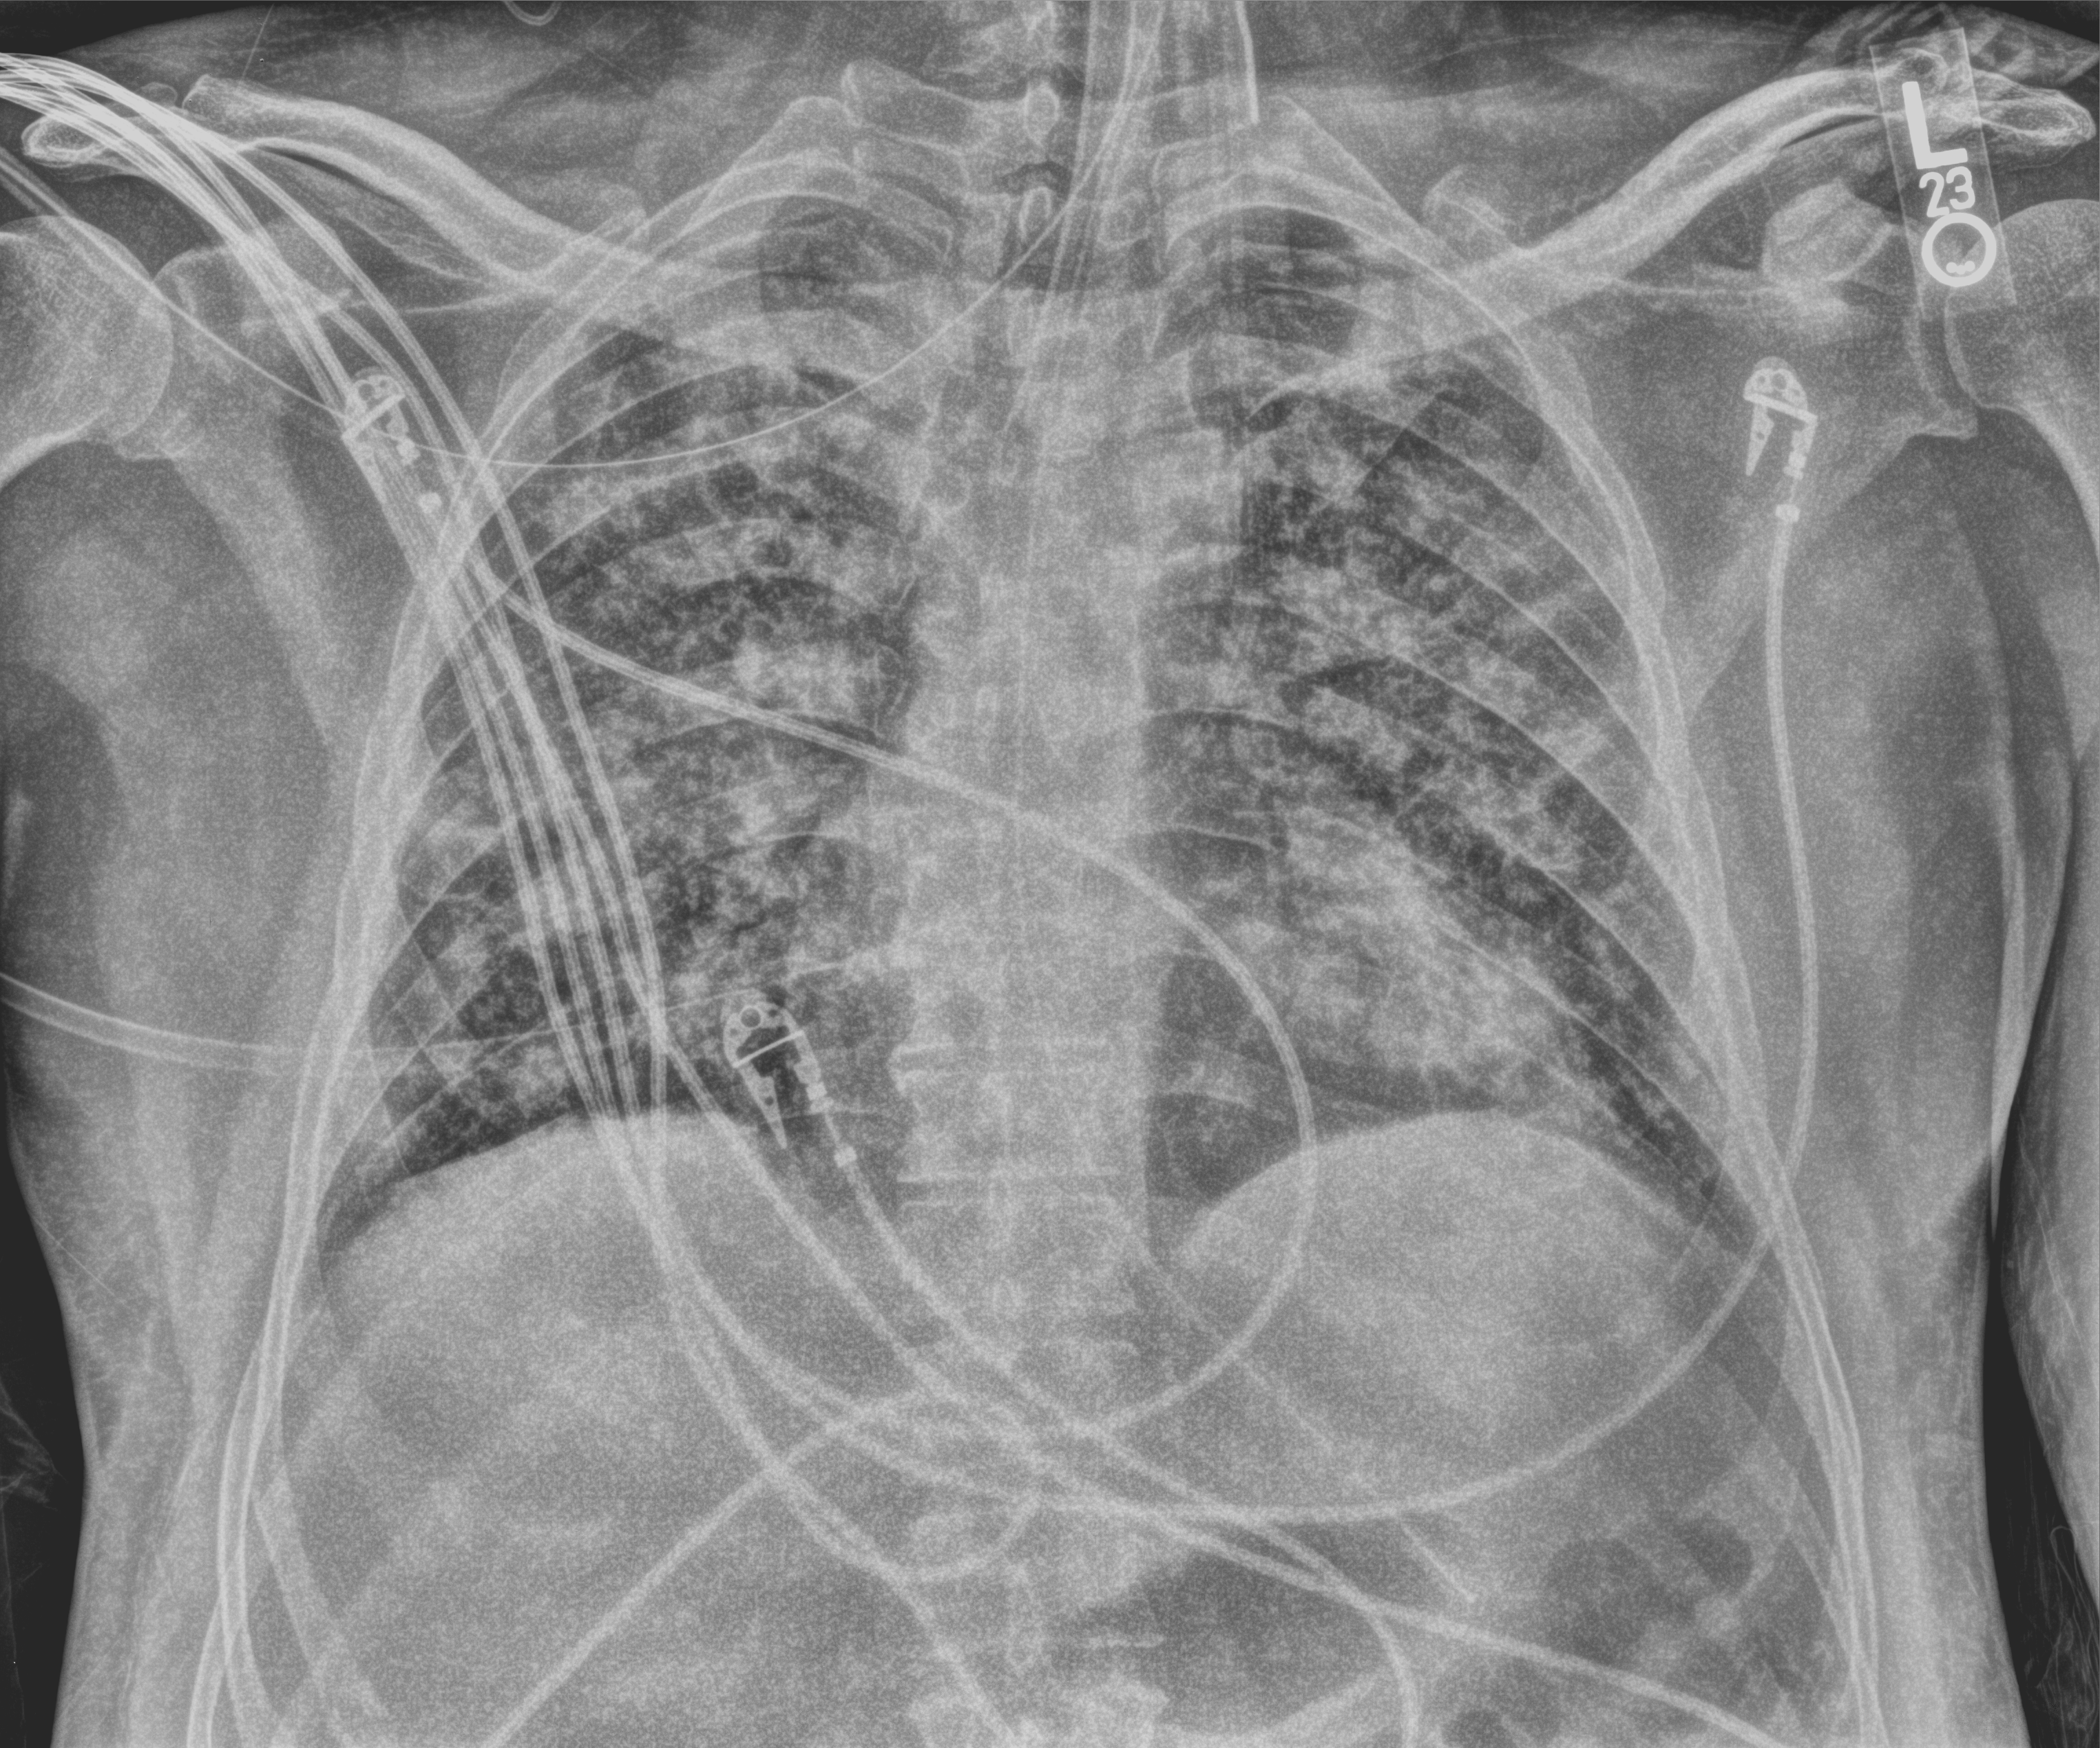
Portable chest radiograph; anteroposterior (AP) projection. Patient hospitalised with COVID-19; male, aged 18–59 years.
Admission-level facts for this patient (not findings on this image; timing relative to this image not recorded):
- mechanically ventilated during this hospital stay: yes
- admitted to intensive care during this hospital stay: yes
- other chronic lung disease (admission record): no